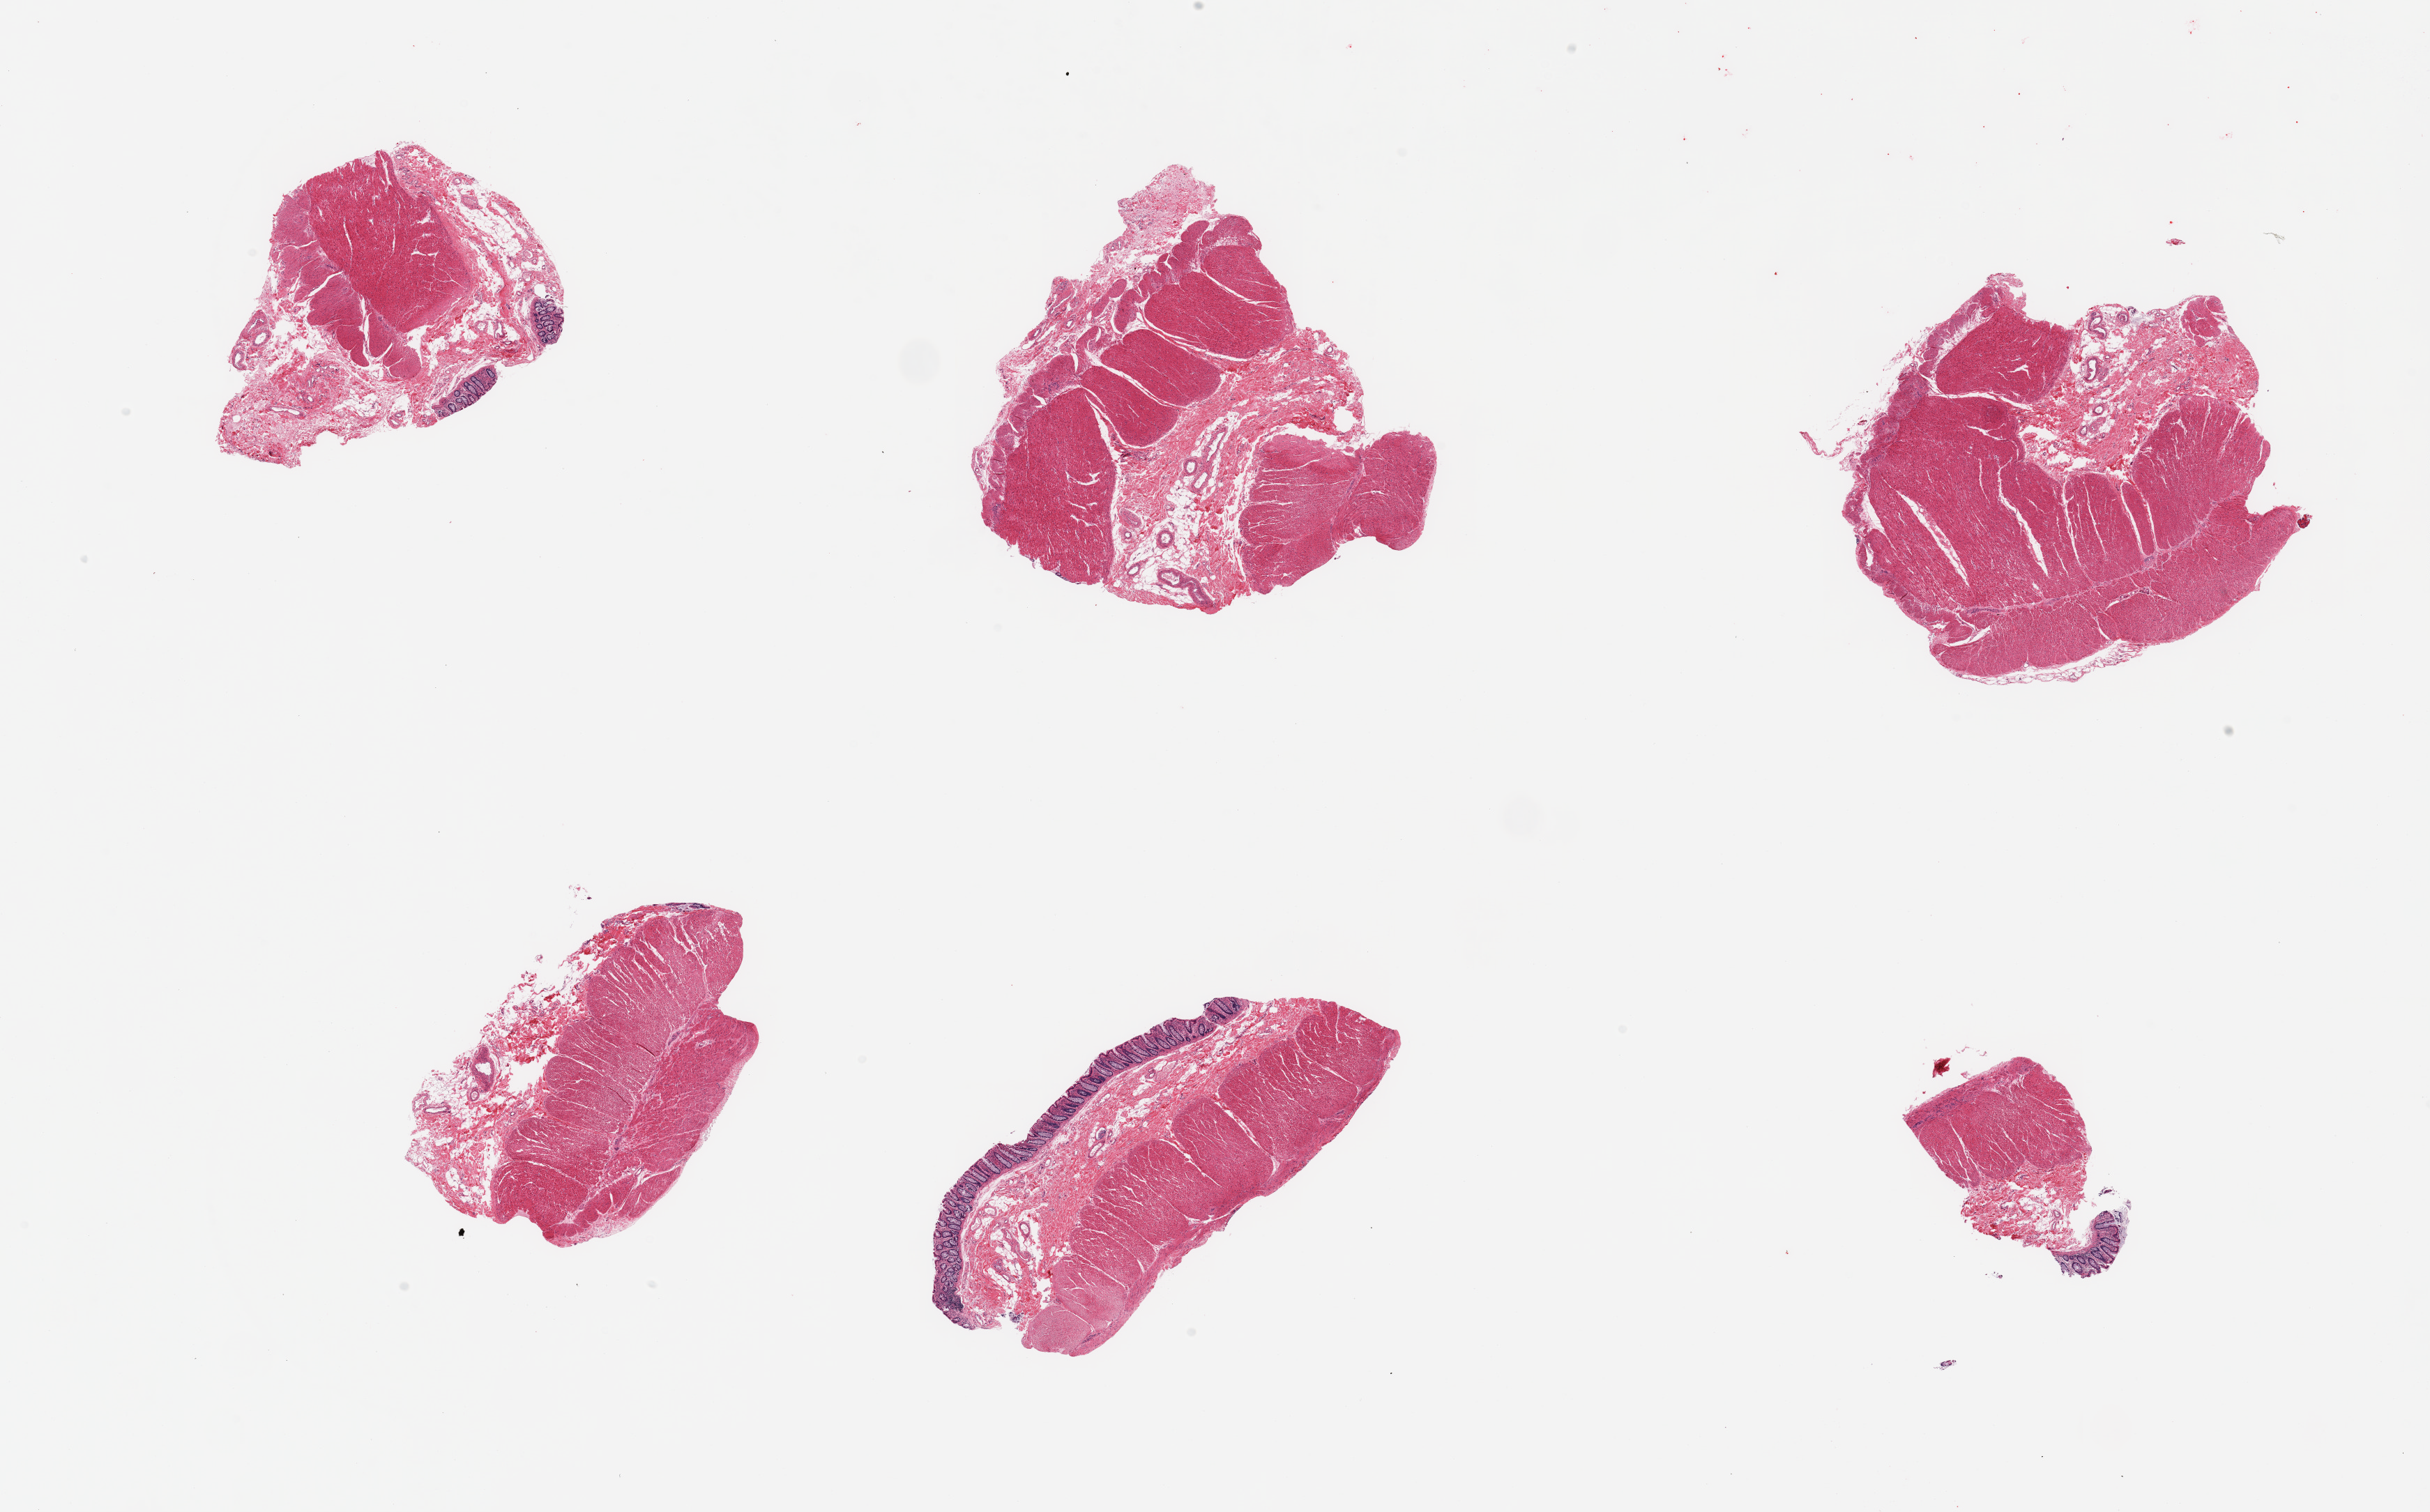
Digitized H&E-stained section, brightfield, a low-resolution overview of the entire scanned area, about 27.6 x 17.2 mm; PAXgene-fixed paraffin-embedded (PFPE) section; target tissue: transverse colon; tissue donor sample.
Pathologist's review note for this sample: 6 pieces, trace mucosa up to ~0.25mm.